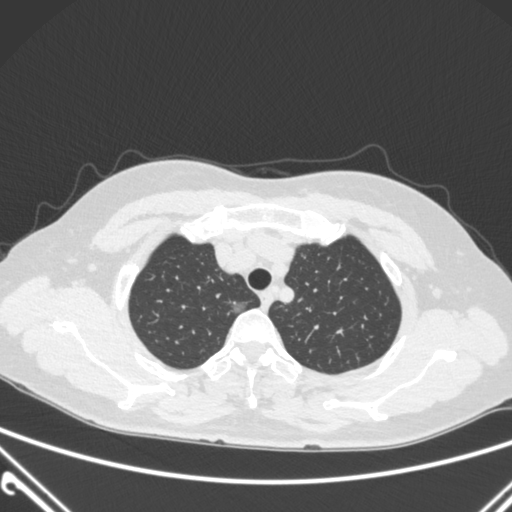
Chest CT, one axial slice. Slice 236 of 300 in the series (ordered by position). Lung window (W 1500 / L -600 HU). 1 mm slice thickness. 512 × 512 image matrix. Female patient, age 54 years. Case-level facts recorded for this patient, not image findings: clinical TNM (as recorded): T1a N0 M0.
Annotated regions visible in this slice (bounding box drawn by a radiologist):
- lung tumour (recorded histology: adenocarcinoma): bounding box [x1, y1, x2, y2] px = [223, 293, 257, 317]